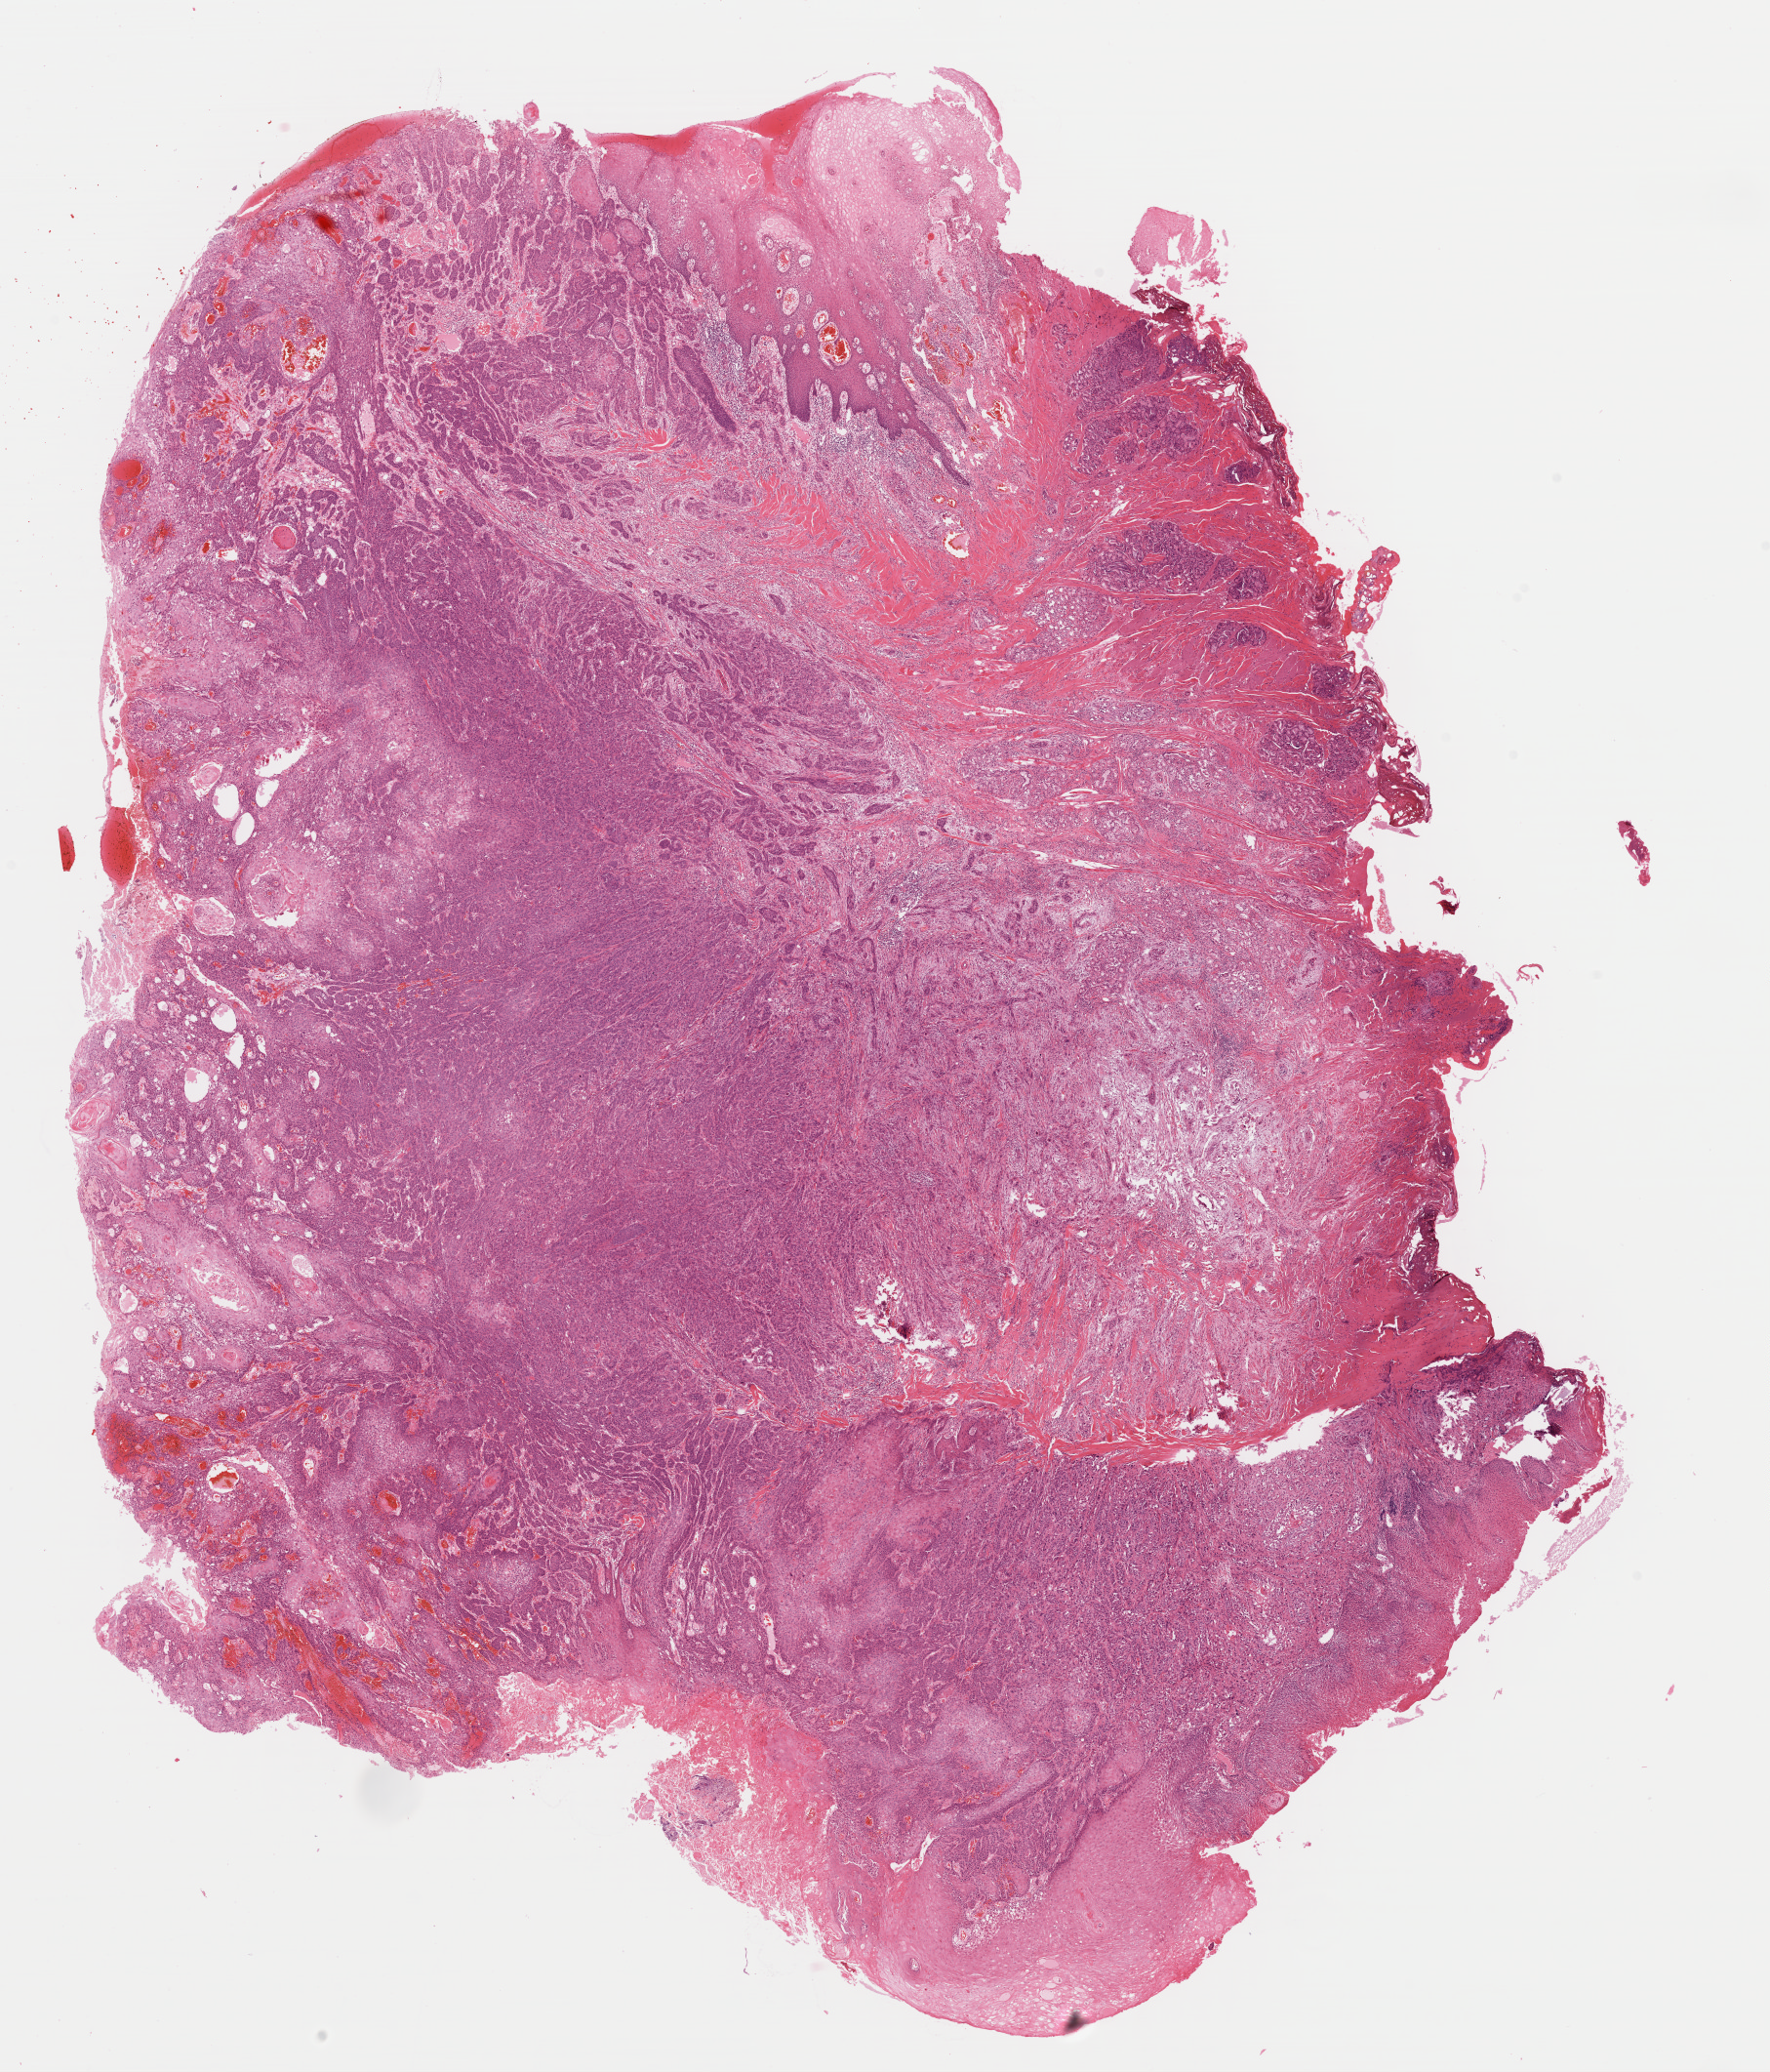
Digitized H&E-stained tissue section (whole slide) — a low-resolution overview of the entire scanned area, about 14.3 x 16.8 mm (slide scanned at 40x); formalin-fixed paraffin-embedded (FFPE) diagnostic section; primary tumour sample from the head and neck. Patient: male, age at initial diagnosis 51 years. Histologic grade: G2 (moderately differentiated).
Diagnosis: Squamous cell carcinoma, keratinizing, NOS (tongue, NOS). Lymph nodes positive (case pathology): 4 of 9 examined. AJCC pathologic stage: IVA (7th edition).